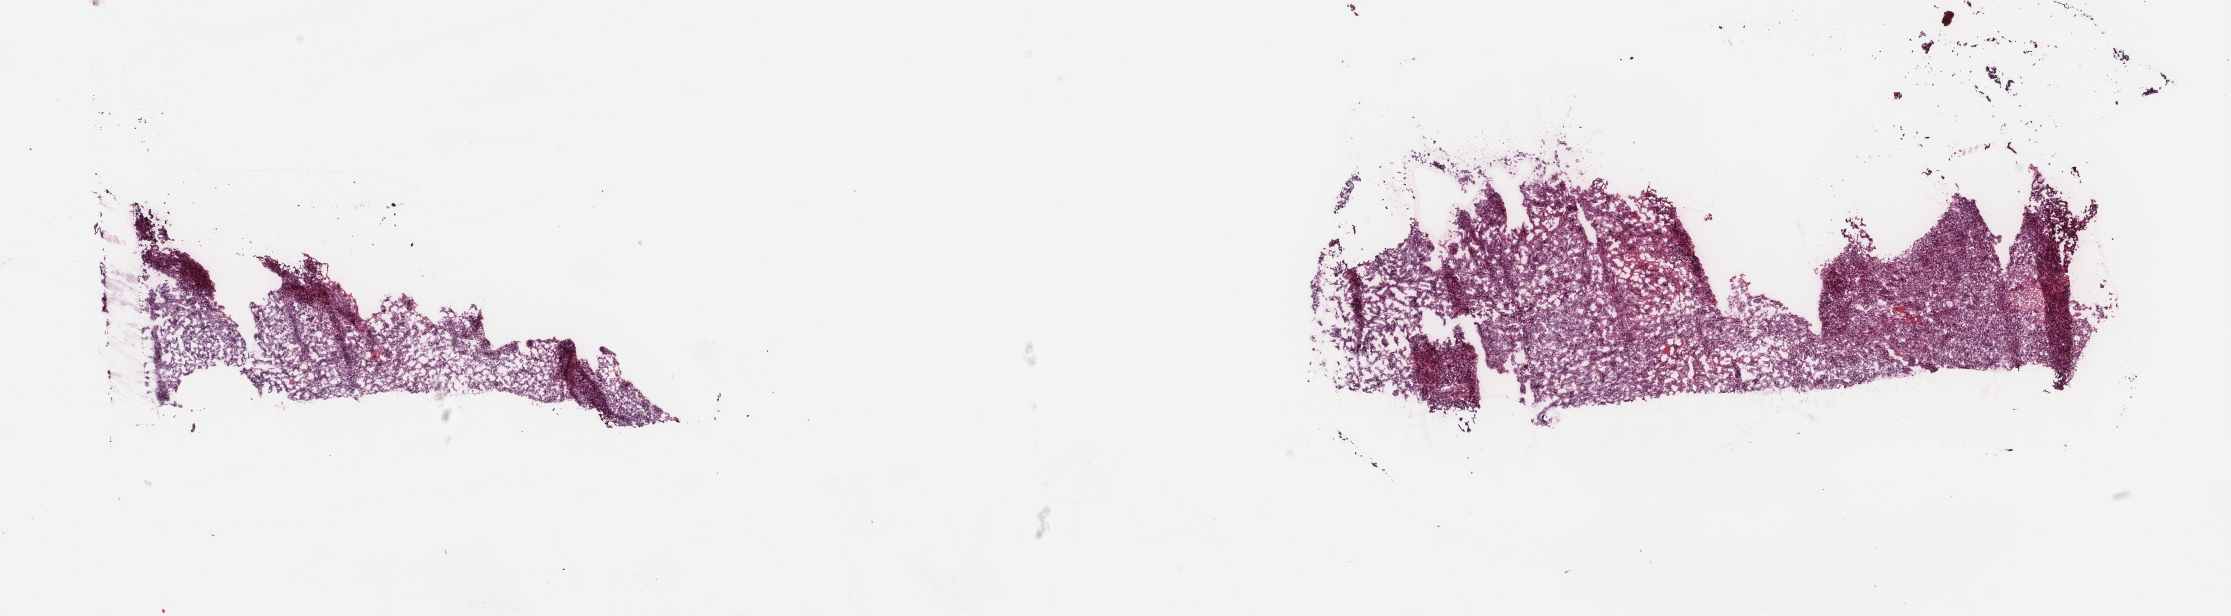
Digitized Hematoxylin and eosin (H&E) stained tissue section (whole slide), shown as a low-resolution overview of the whole scanned area (about 17.7 x 4.9 mm). Frozen section from the top of the tissue portion. Primary tumour sample from the uterus. Patient: female, age at initial diagnosis 77 years. Slide review estimates, as recorded: tumour cells 88%, tumour nuclei 96%.
Histologic diagnosis: Endometrioid adenocarcinoma, NOS (endometrium).